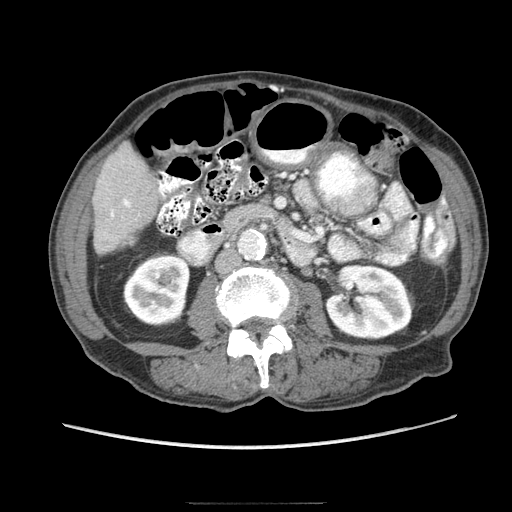
Contrast-enhanced abdominal CT (liver protocol), one axial slice; position 21 of 83 along the scan axis; reconstruction kernel STANDARD; 140 kVp; soft-tissue window (W 400 / L 40 HU); 2.5 mm slice thickness; 512 × 512 image matrix, field of view 360 × 360 mm. Case-level facts recorded for this patient, not image findings: diagnosis: hepatocellular carcinoma (patient treated with transarterial chemoembolisation; whether this scan precedes or follows treatment is not stated here); TNM stage (as recorded): Stage-I; Child-Pugh class: A.
Structures marked on this image (semi-automatic segmentation, software-assisted and operator-edited):
- liver parenchyma outside the tumour (the mass and vessels are separate outlines, so this box may not span the whole liver): bounding box <92,144,158,254> (left, top, right, bottom; pixels)
- liver vessels: <111,199,131,217>